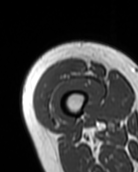
MRI of an extremity soft-tissue mass, one axial slice; position 12 of 99 along the scan axis; MR volume resampled by the dataset authors to the PET/CT grid (not the native acquisition matrix); 3.27 mm slice thickness; 138 × 172 image matrix. Female patient. From the clinical record (not read from this slice): histological type: pleiomorphic undifferentiated sarcoma; grade: high; site of the primary tumour: right quadricep.
Outlined on this slice (expert contour drawn on MRI and transferred to this co-registered scan by the dataset authors):
- gross tumour volume including surrounding oedema: bounding box (x1, y1, x2, y2) in pixels: (35, 59, 88, 110)